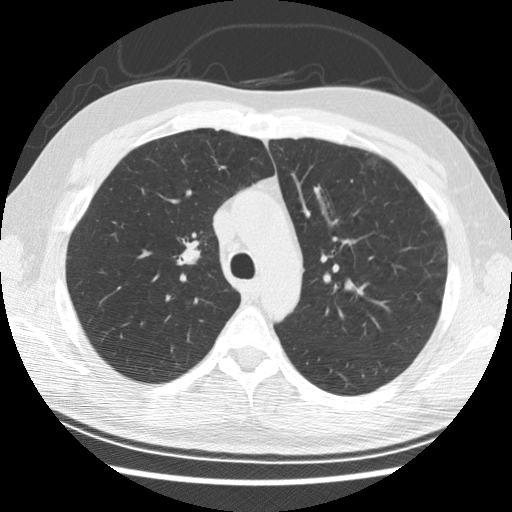
Chest CT (low-dose screening protocol), one axial image; baseline screening round; lung window (W 1500 / L -600 HU); 2.5 mm slice thickness; slice 85 of 278 in the series; 512 × 512 image matrix. Male participant, aged 57 years at enrolment.
- Expert-annotated lung lesion, box from (x=163, y=221) to (x=220, y=281) px.
- The screening reader recorded 6 non-calcified nodules or masses ≥4 mm on this exam (right middle lobe, right middle lobe, right lower lobe, right middle lobe, right middle lobe, right lower lobe); which of them this box marks is not recorded.
- Lung cancer was diagnosed 766 days after this screen (after the second annual screen): adenocarcinoma, NOS, right upper lobe, poorly differentiated (G3), stage IB (AJCC 6th edition), 25 mm at pathology.